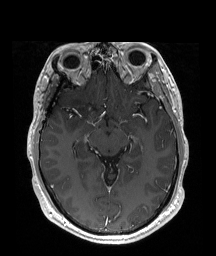
Brain MRI from a brain-tumour surgery series, one axial slice. Slice 114 of 192 in the series (ordered by position). T1-weighted post-contrast. 216 × 256 image matrix, field of view 219 × 260 mm. Case-level facts recorded for this patient, not image findings: histopathology: Astrocytoma; WHO grade: 2; IDH mutation: yes; tumour location: Right Insular.
Annotated regions visible in this slice (outlined manually by an expert reader):
- tumour: box from (x=67, y=98) to (x=93, y=133) px